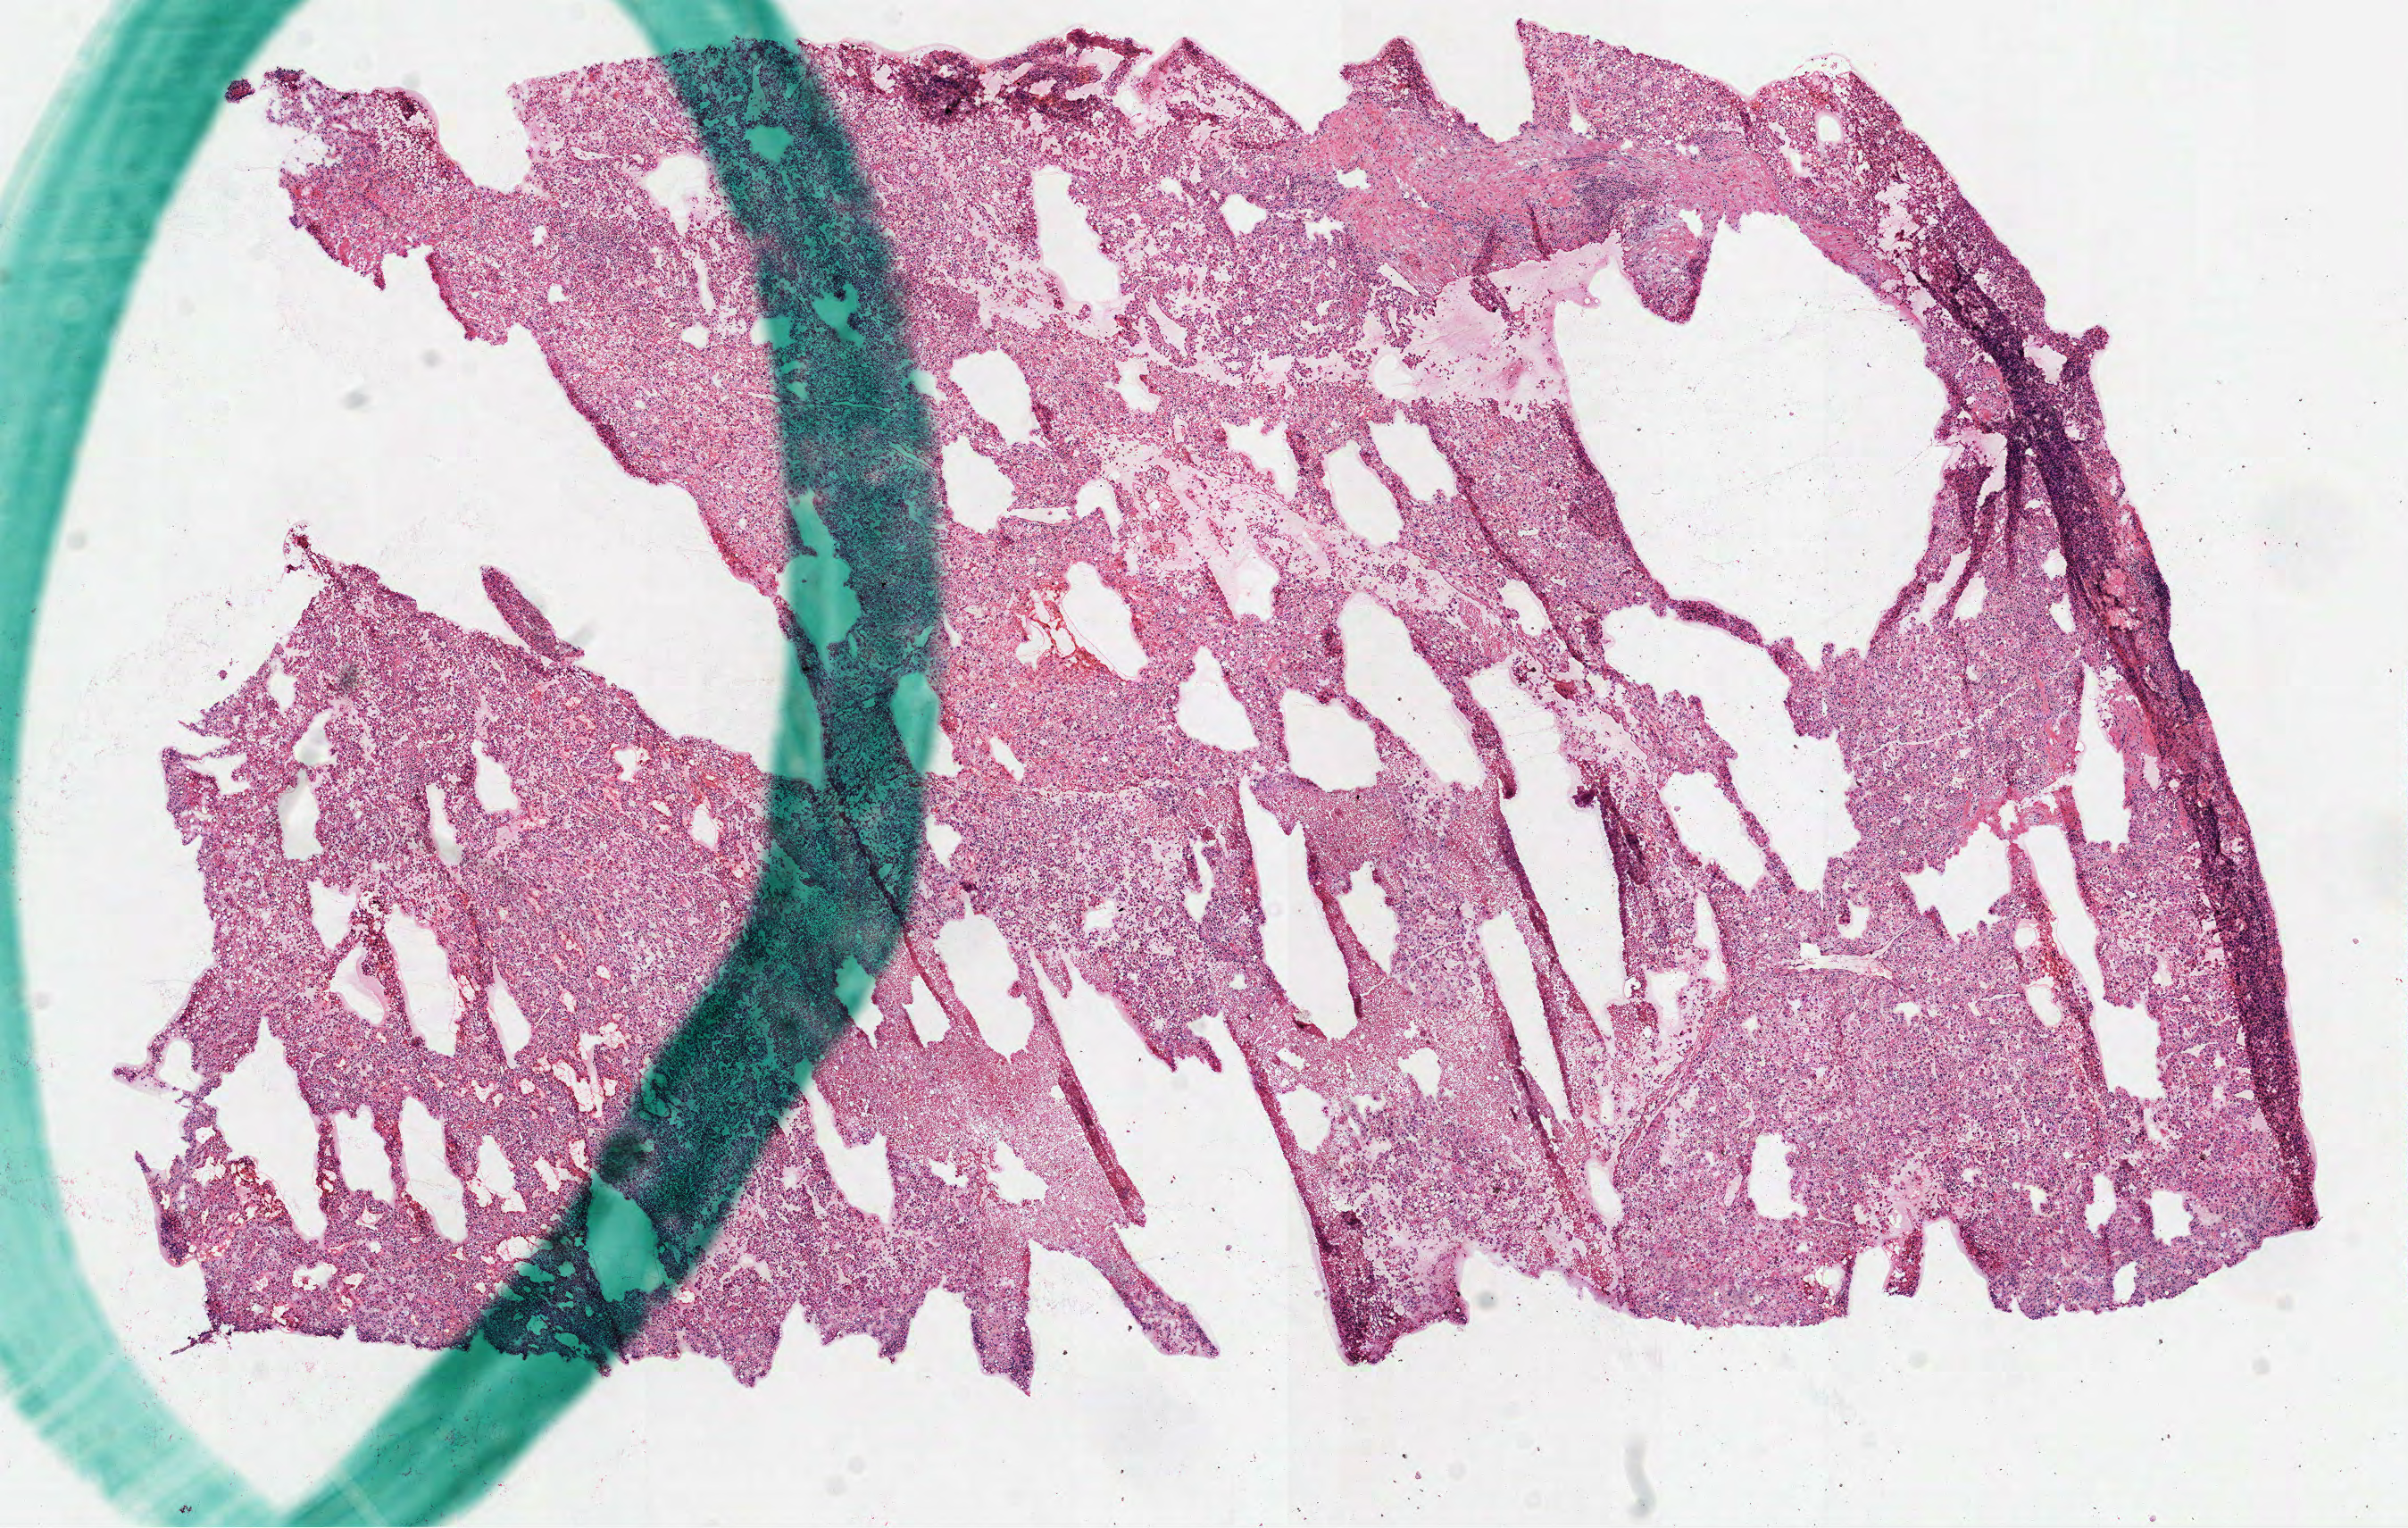
Whole-slide histology image, H&E-stained — a low-resolution overview of the entire scanned area, about 10.9 x 6.9 mm (slide scanned at 40x); frozen section; primary tumour sample from the kidney. Patient: male, age at initial diagnosis 77 years. Histologic grade: G4 (undifferentiated). Composition of this section per pathologist review: tumour cells 90%, tumour nuclei 80%, normal cells 0%, stromal cells 10%, necrosis 0%.
• pathologic diagnosis: Clear cell adenocarcinoma, NOS
• AJCC pathologic stage: I (6th edition)
• laterality: right